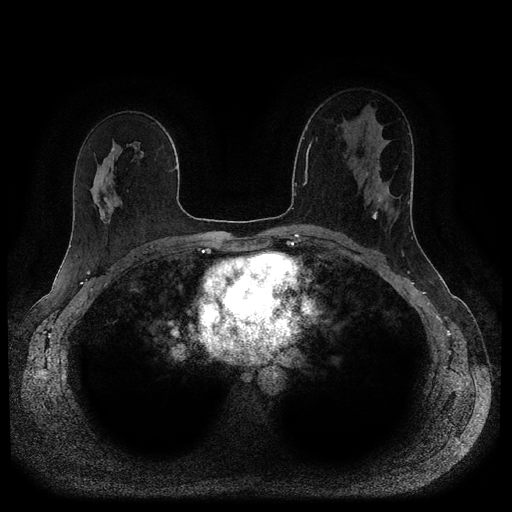
Breast MRI (dynamic contrast-enhanced, multi-phase), one axial slice. Slice 58 of 116 in the series (ordered by position). Dynamic contrast-enhanced series, time point 2 of 5 at this slice position (early post-contrast). 1.5 T. TE 2.6 ms, TR 5.3 ms. 512 × 512 image matrix, field of view 350 × 350 mm. Female patient, age 45 years.
Annotated regions visible in this slice (semi-automatic segmentation, software-assisted and operator-edited):
- breast lesion (labelled 'tumour' in the annotation; benign lesions carry a separate 'benign' label): box from (x=374, y=193) to (x=388, y=209) px